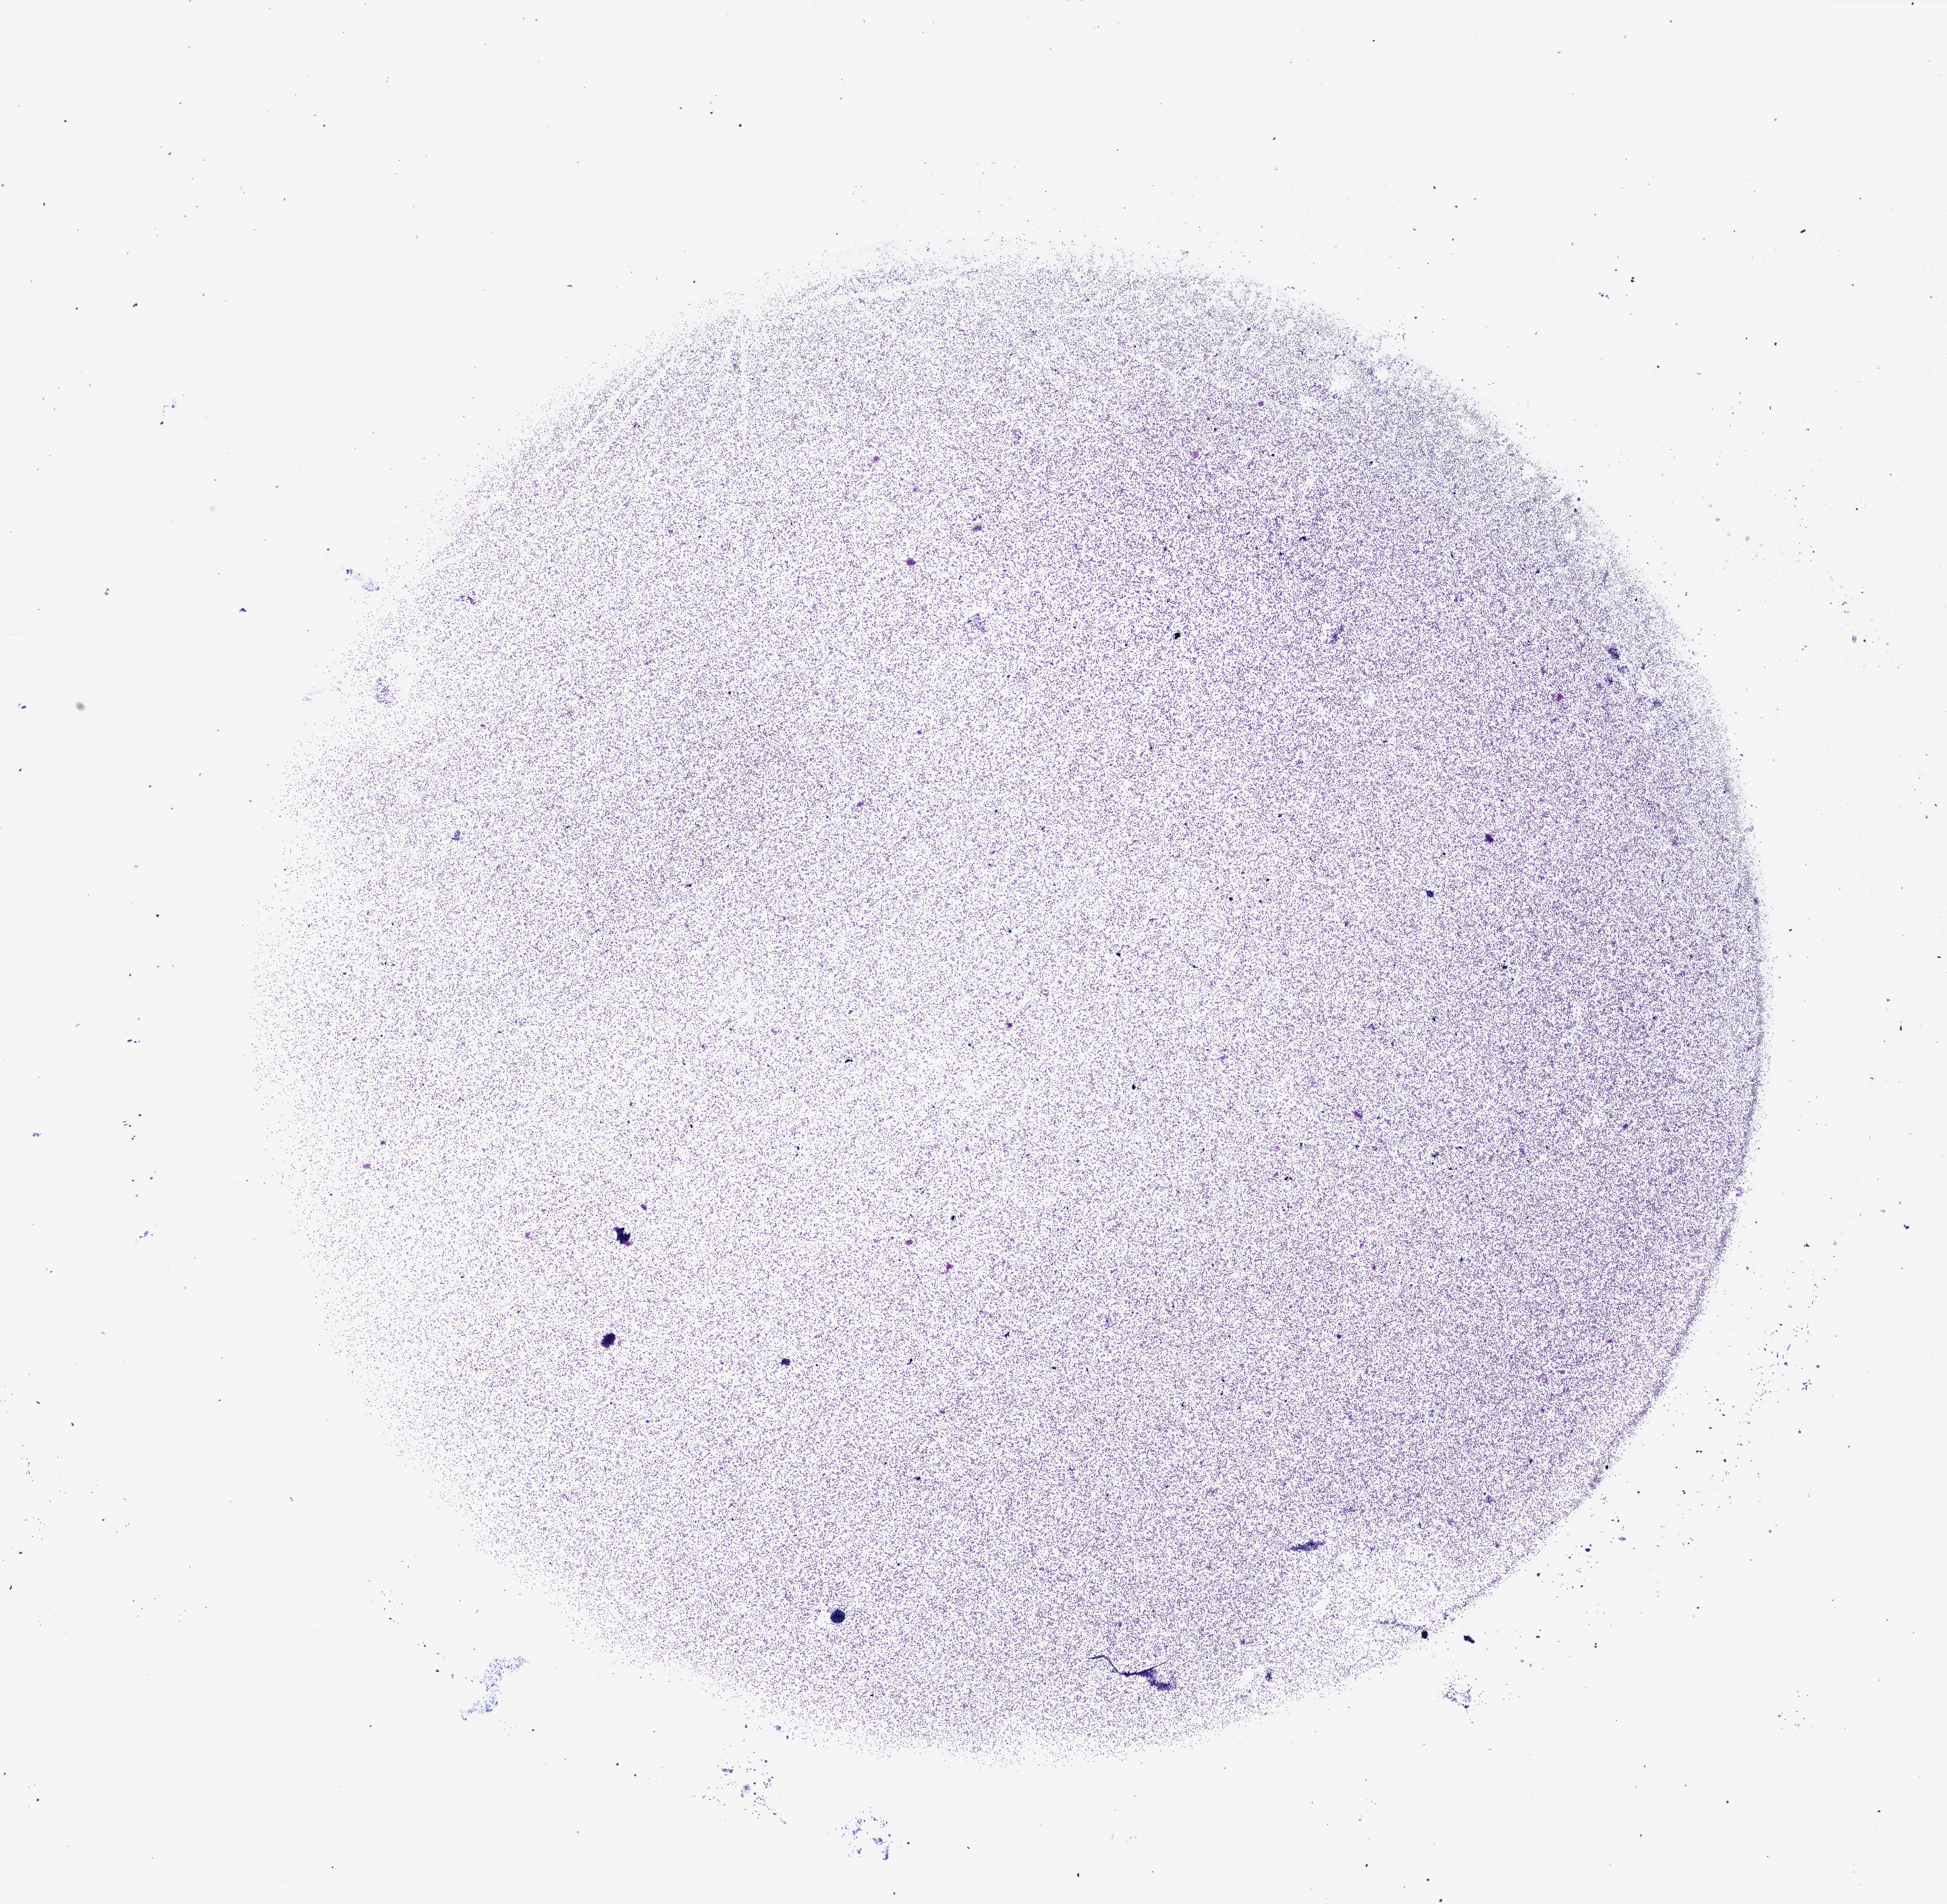
Digitized H&E-stained tissue section (whole slide), low-resolution overview of the scanned area, about 22.8 x 22.3 mm. Bone marrow (leukaemic) sample. 56-year-old female patient. Blasts: 95%.
- WHO classification: AML with maturation
- diagnosis: Acute Myeloid Leukemia
- FAB classification: M2